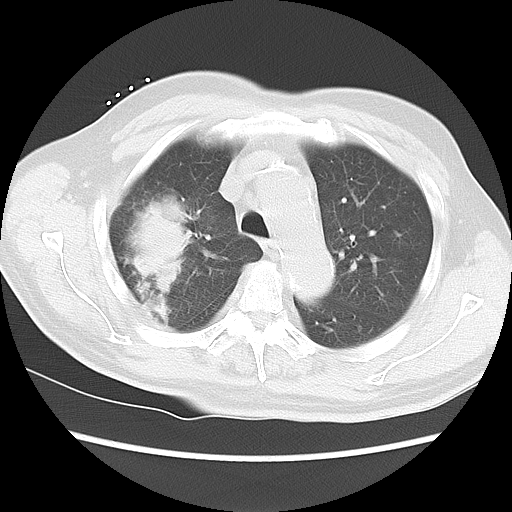
Chest CT, one axial slice. Position 14 of 15 along the scan axis. Reconstruction kernel LUNG. 120 kVp. Lung window (W 1500 / L -600 HU). 5 mm slice thickness. 512 × 512 image matrix, field of view 350 × 350 mm. Male patient, age 68 years. From the clinical record (not read from this slice): clinical TNM (as recorded): T4 N3 M0.
Structures marked on this image (rectangle marked by the reading radiologist):
- lung tumour (recorded histology: squamous cell carcinoma): bounding box (x1, y1, x2, y2) in pixels: (125, 189, 193, 327)